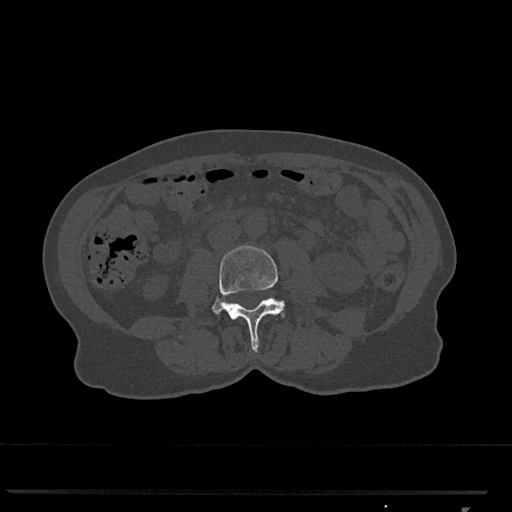
CT including the spine, one axial slice. Slice 268 of 793 in the series (ordered by position). Reconstruction kernel Br40s/3. 120 kVp. Bone window (W 1800 / L 400 HU). 0.5 mm slice thickness. 512 × 512 image matrix, field of view 380 × 380 mm. Patient: female, 62 years. Case-level facts recorded for this patient, not image findings: primary cancer: renal.
Annotated regions visible in this slice (semi-automatically segmented with operator editing):
- L3 vertebra: bounding box (x1, y1, x2, y2) in pixels: (211, 245, 285, 352)